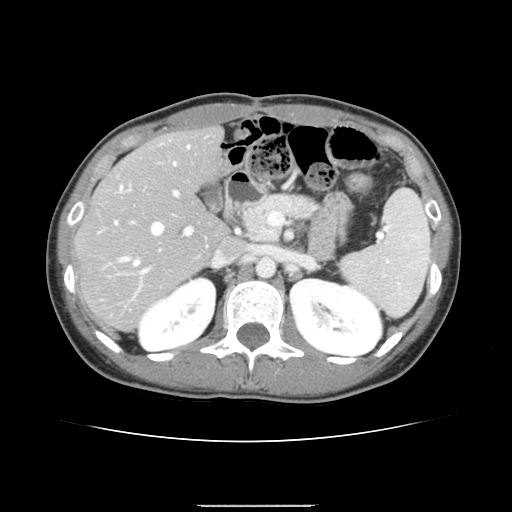
Contrast-enhanced abdominal CT, one axial slice. Position 87 of 150 along the scan axis. 120 kVp. Intravenous contrast given. Soft-tissue window (W 400 / L 40 HU). 2.5 mm slice thickness. 512 × 512 image matrix, field of view 324 × 324 mm. Female patient, age 32 years. Case-level facts recorded for this patient, not image findings: diagnosis: colorectal cancer liver metastases, imaged before liver resection; multiple liver metastases: yes; largest metastasis: 0.7 cm; disease in both lobes: no.
Outlined on this slice (manually delineated by an expert):
- hepatic veins: bounding box (x1, y1, x2, y2) in pixels: (115, 145, 189, 264)
- liver: (78, 129, 227, 330)
- planned liver remnant (the part of the liver to remain after resection): (78, 129, 226, 277)
- portal vein (with intrahepatic branches): (120, 190, 192, 295)